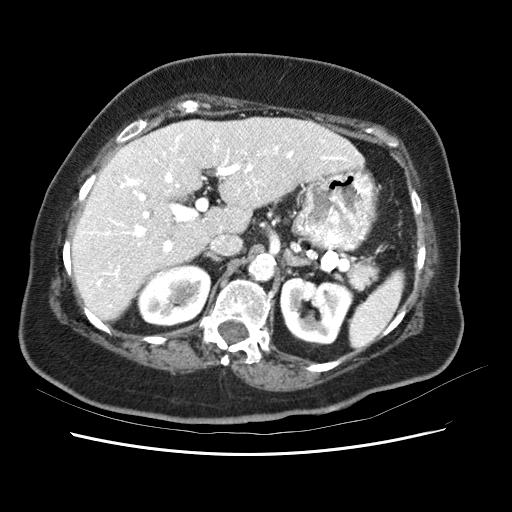
Contrast-enhanced abdominal CT (liver protocol), one axial slice. Slice 37 of 62 in the series (ordered by position). 120 kVp. Soft-tissue window (W 400 / L 40 HU). 512 × 512 image matrix. From the clinical record (not read from this slice): diagnosis: hepatocellular carcinoma (patient treated with transarterial chemoembolisation; whether this scan precedes or follows treatment is not stated here); TNM stage (as recorded): Stage-I; Child-Pugh class: B.
Structures marked on this image (semi-automatic segmentation, software-assisted and operator-edited):
- liver parenchyma outside the tumour (the mass and vessels are separate outlines, so this box may not span the whole liver): box from (x=72, y=116) to (x=366, y=322) px
- liver vessels: (x=75, y=134)–(x=355, y=301)